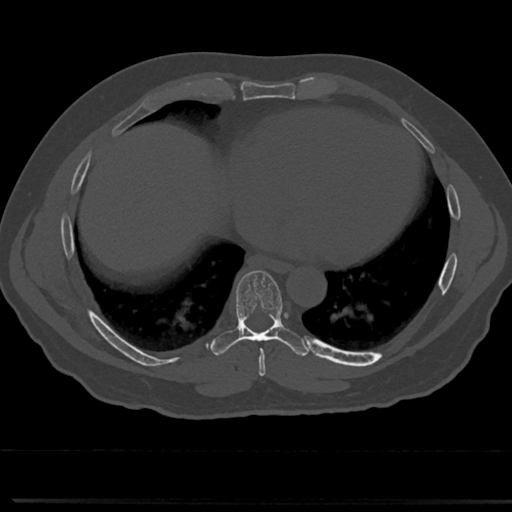
CT including the spine, one axial slice. Position 362 of 817 along the scan axis. Reconstruction kernel Br40s/3. 120 kVp. Bone window (W 1800 / L 400 HU). 0.5 mm slice thickness. 512 × 512 image matrix. Male patient, age 61 years. Case-level facts recorded for this patient, not image findings: primary cancer: prostate.
Outlined on this slice (semi-automatic segmentation, software-assisted and operator-edited):
- T7 vertebra: bounding box (x1, y1, x2, y2) in pixels: (237, 272, 286, 360)
- T8 vertebra: (237, 272, 283, 336)